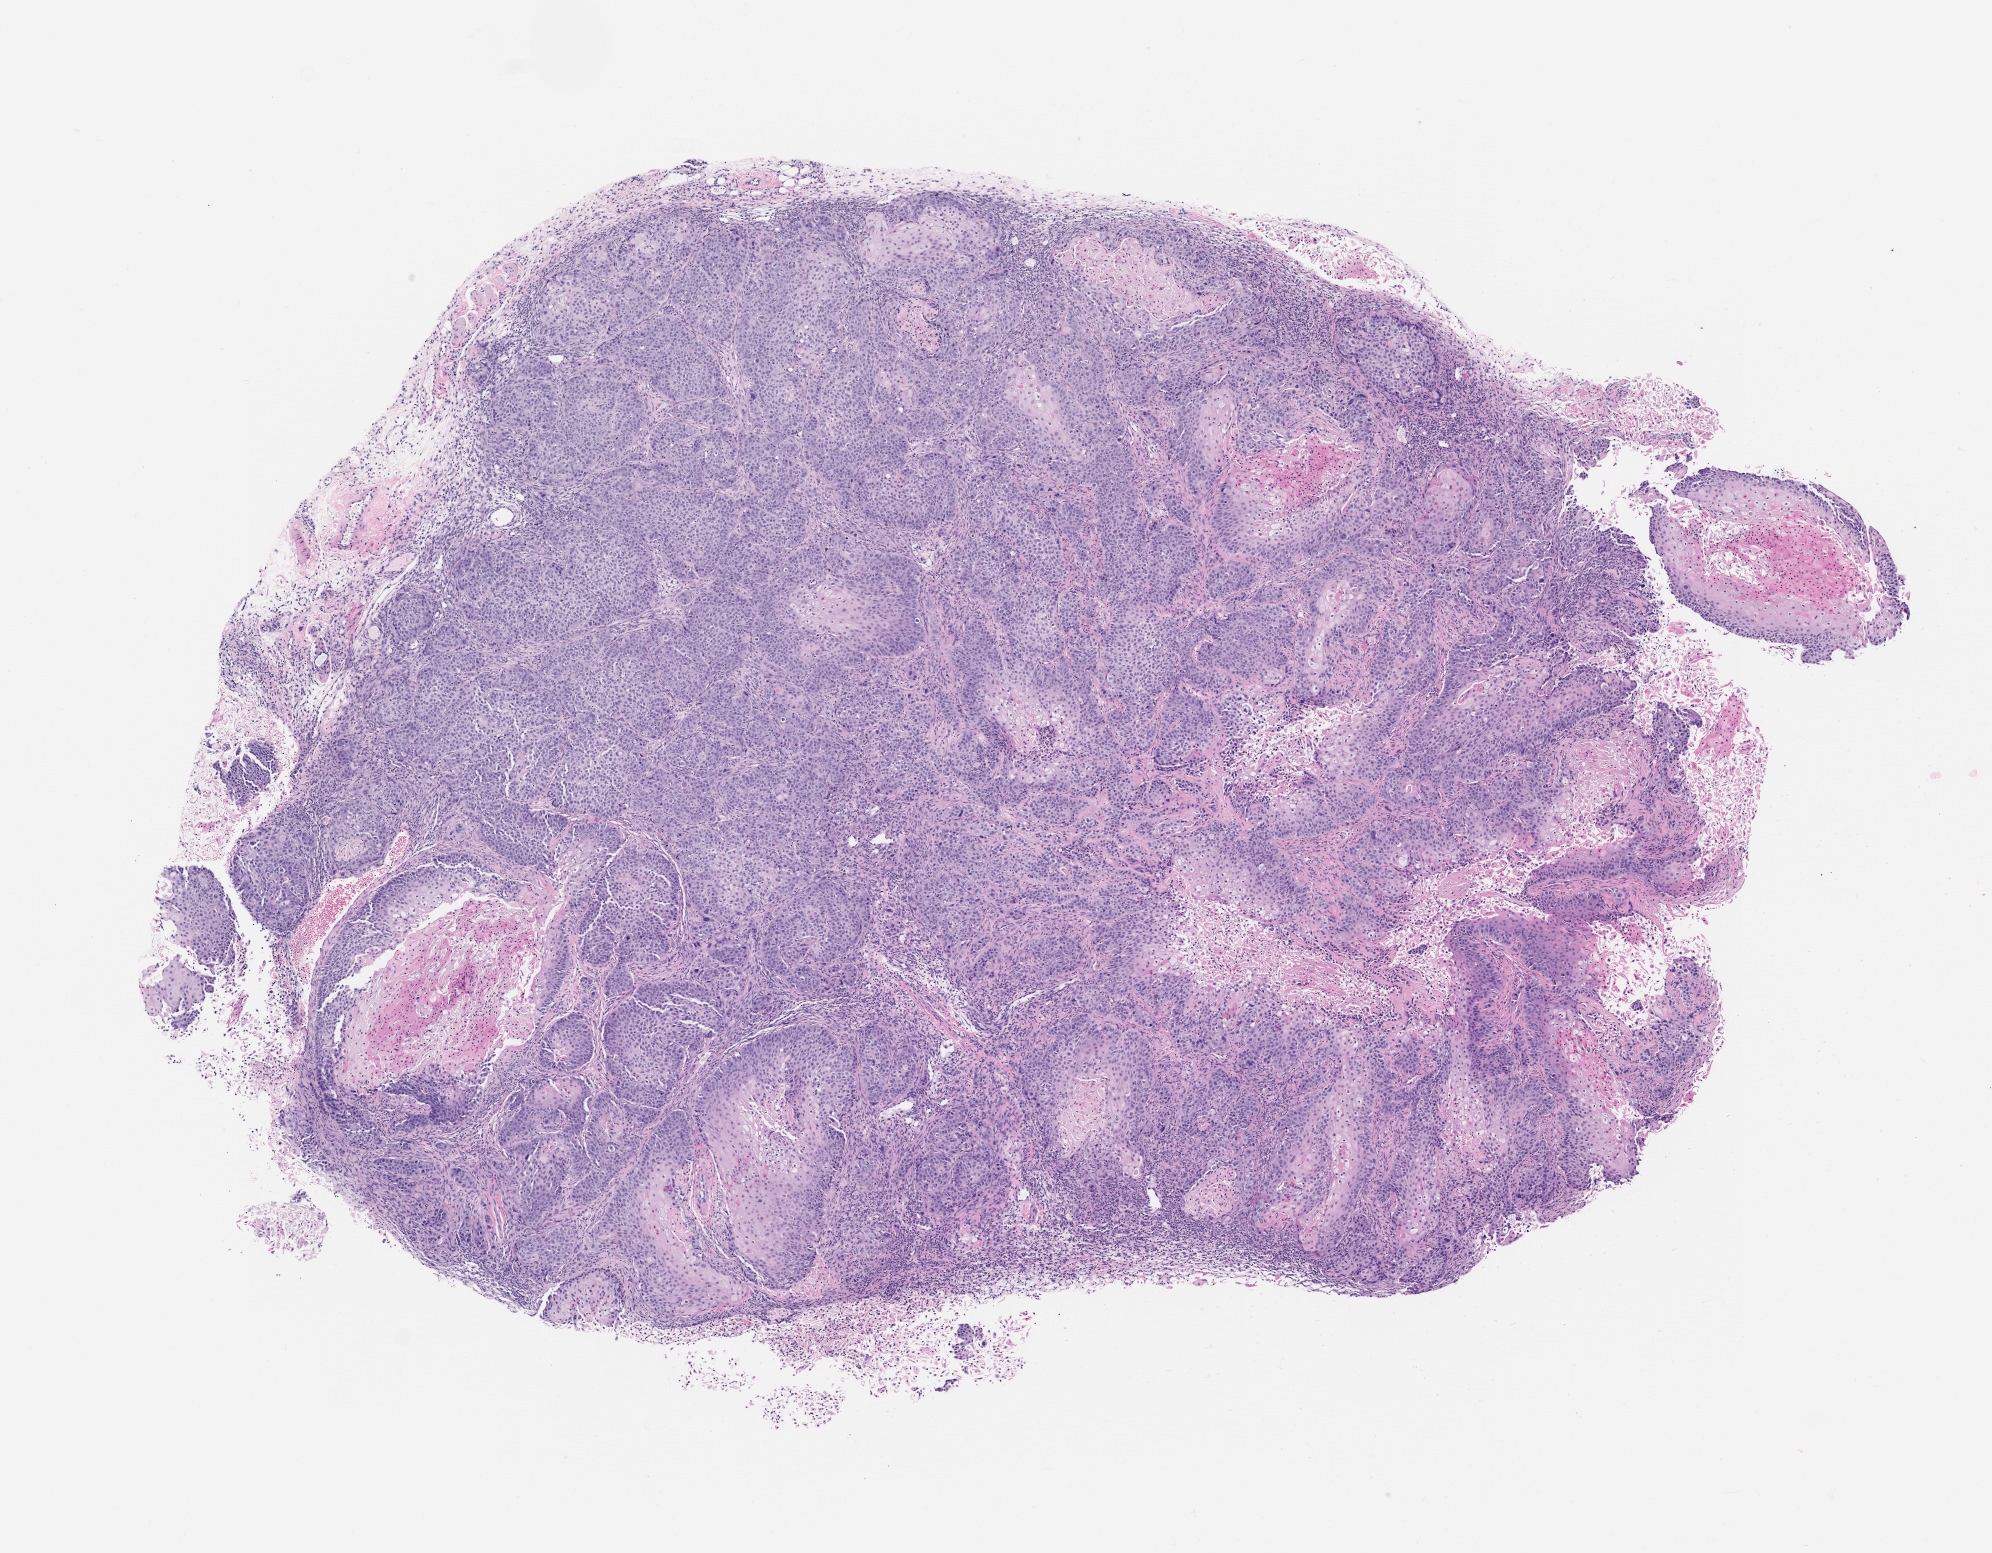
Whole-slide image, hematoxylin and eosin (H&E): patient-derived xenograft (human tumor grown in a mouse), passage 1 — shown as a low-resolution overview of the whole scanned area (about 8.0 x 6.2 mm), FFPE section, originating tumor site category: lung.
Originating patient diagnosis: Lung Squamous Cell Carcinoma.